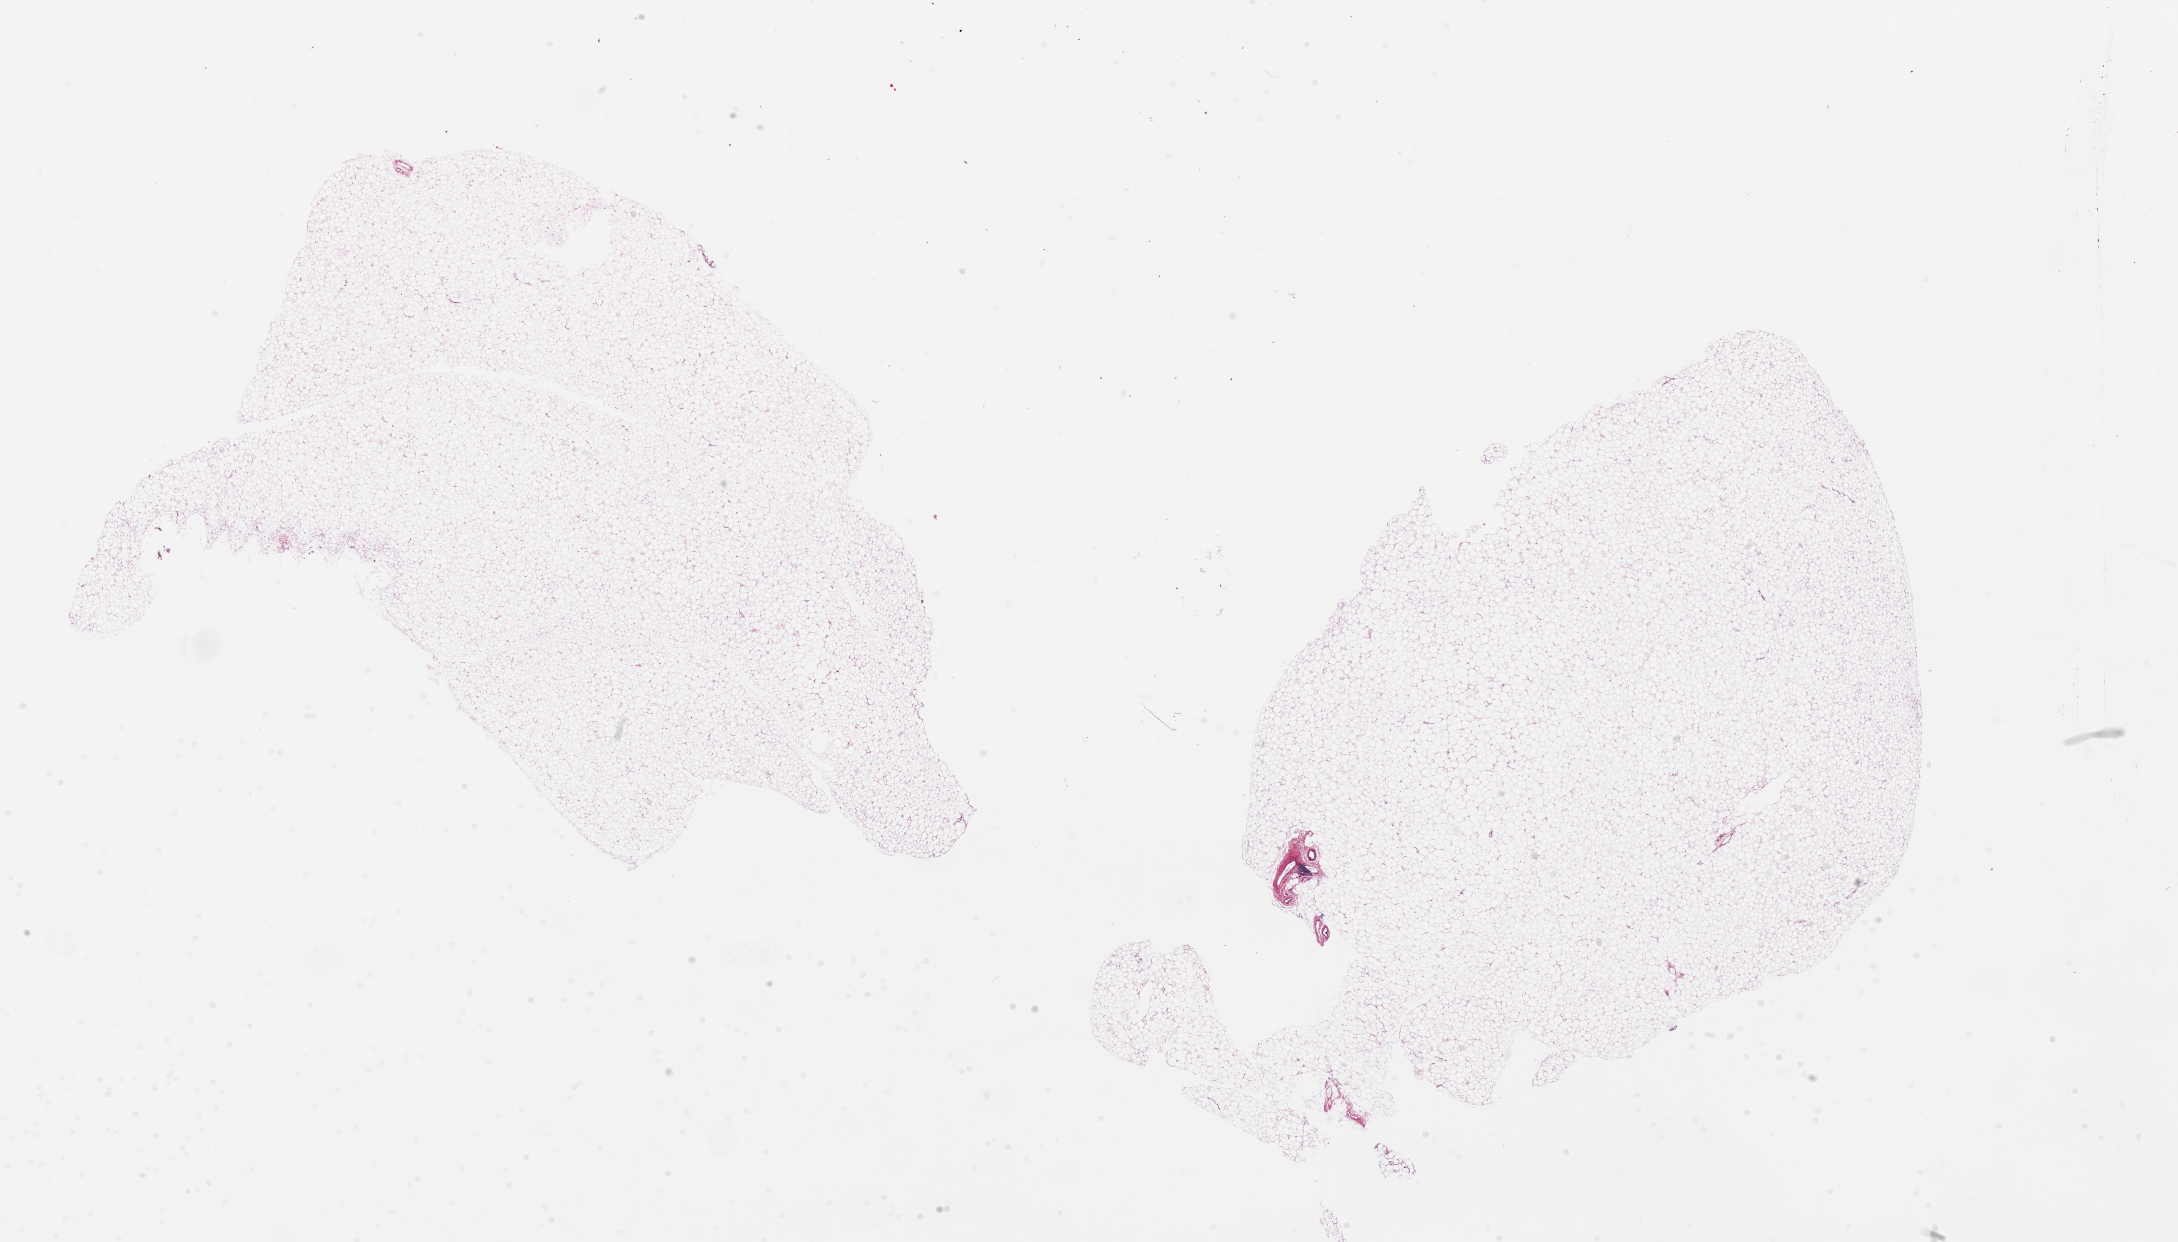
Hematoxylin and eosin (H&E) whole-slide image, low-resolution overview of the scanned area, about 34.5 x 19.6 mm (slide scanned at 20x), PAXgene-fixed, paraffin-embedded tissue, section of omentum (target tissue), tissue donor sample.
Reviewer comment on this tissue sample: 2 pieces, focal perivascular collection of lymphocytes.